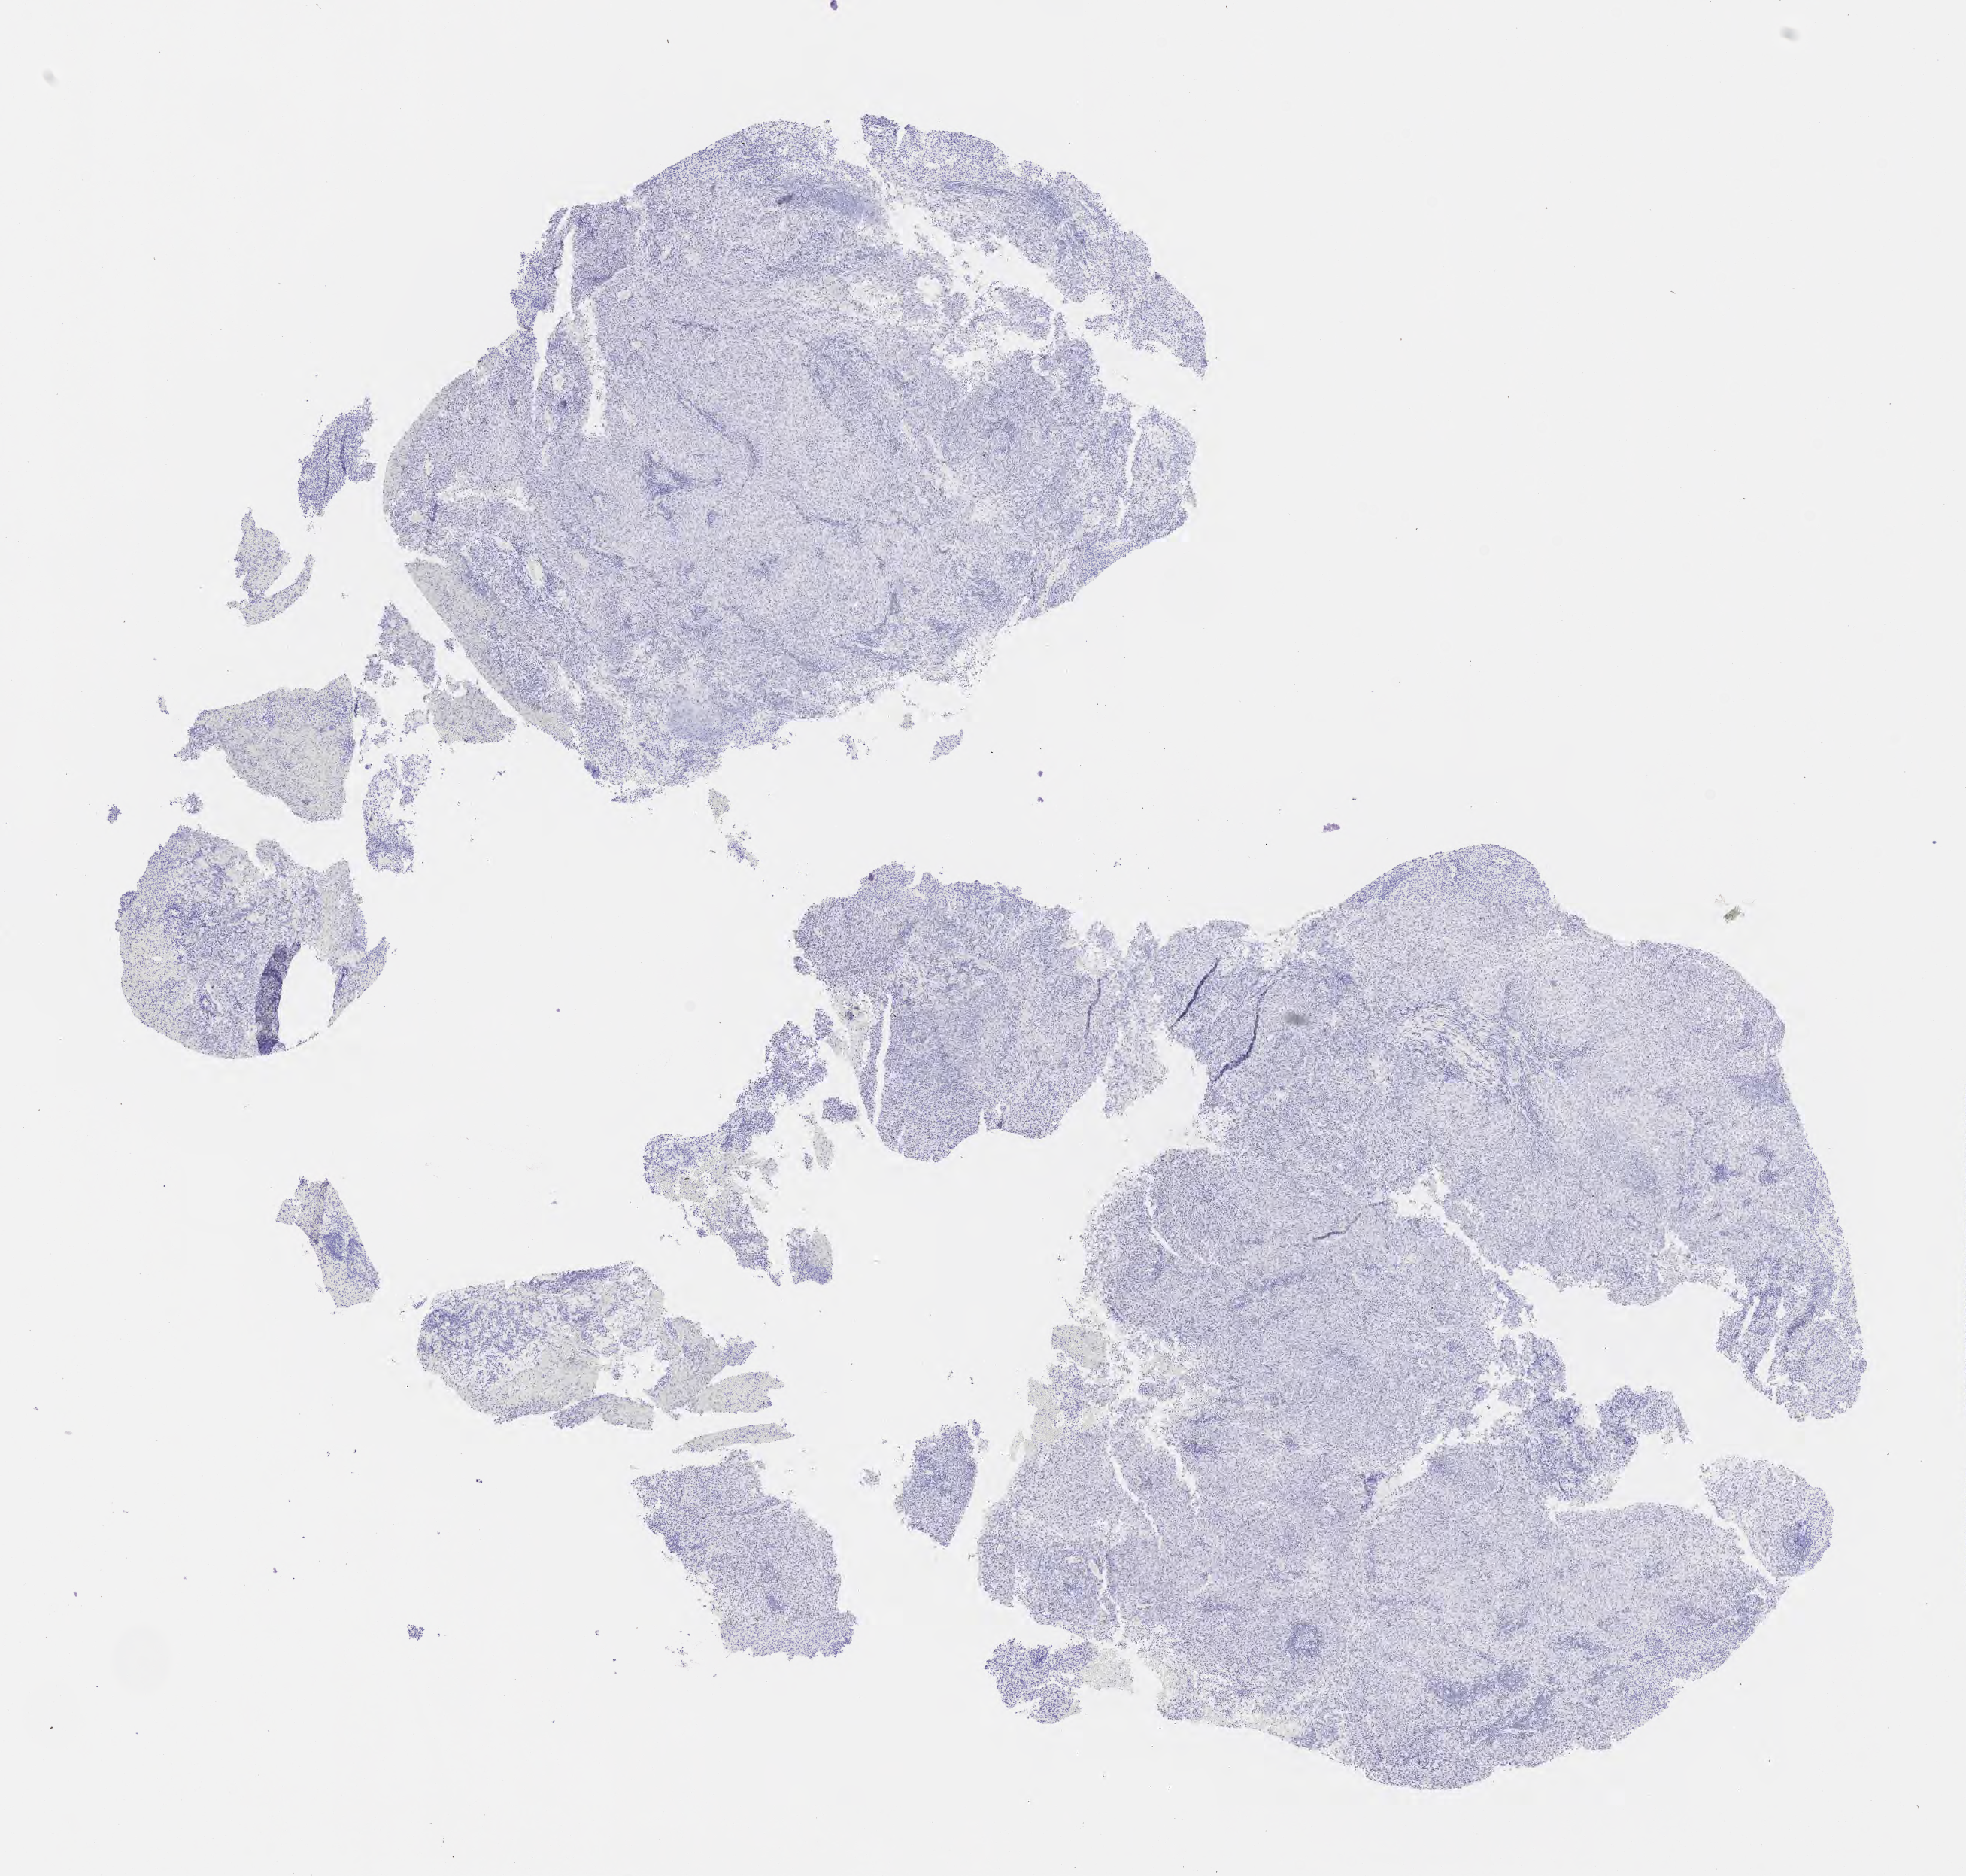
IHC for p40, whole-slide image — whole scanned area (about 10.6 x 10.1 mm) shown as a low-resolution overview. Tumor tissue. Site: cervix. Female patient, 70 years old.
• histologic diagnosis: Squamous cell carcinoma, large cell, nonkeratinizing, NOS